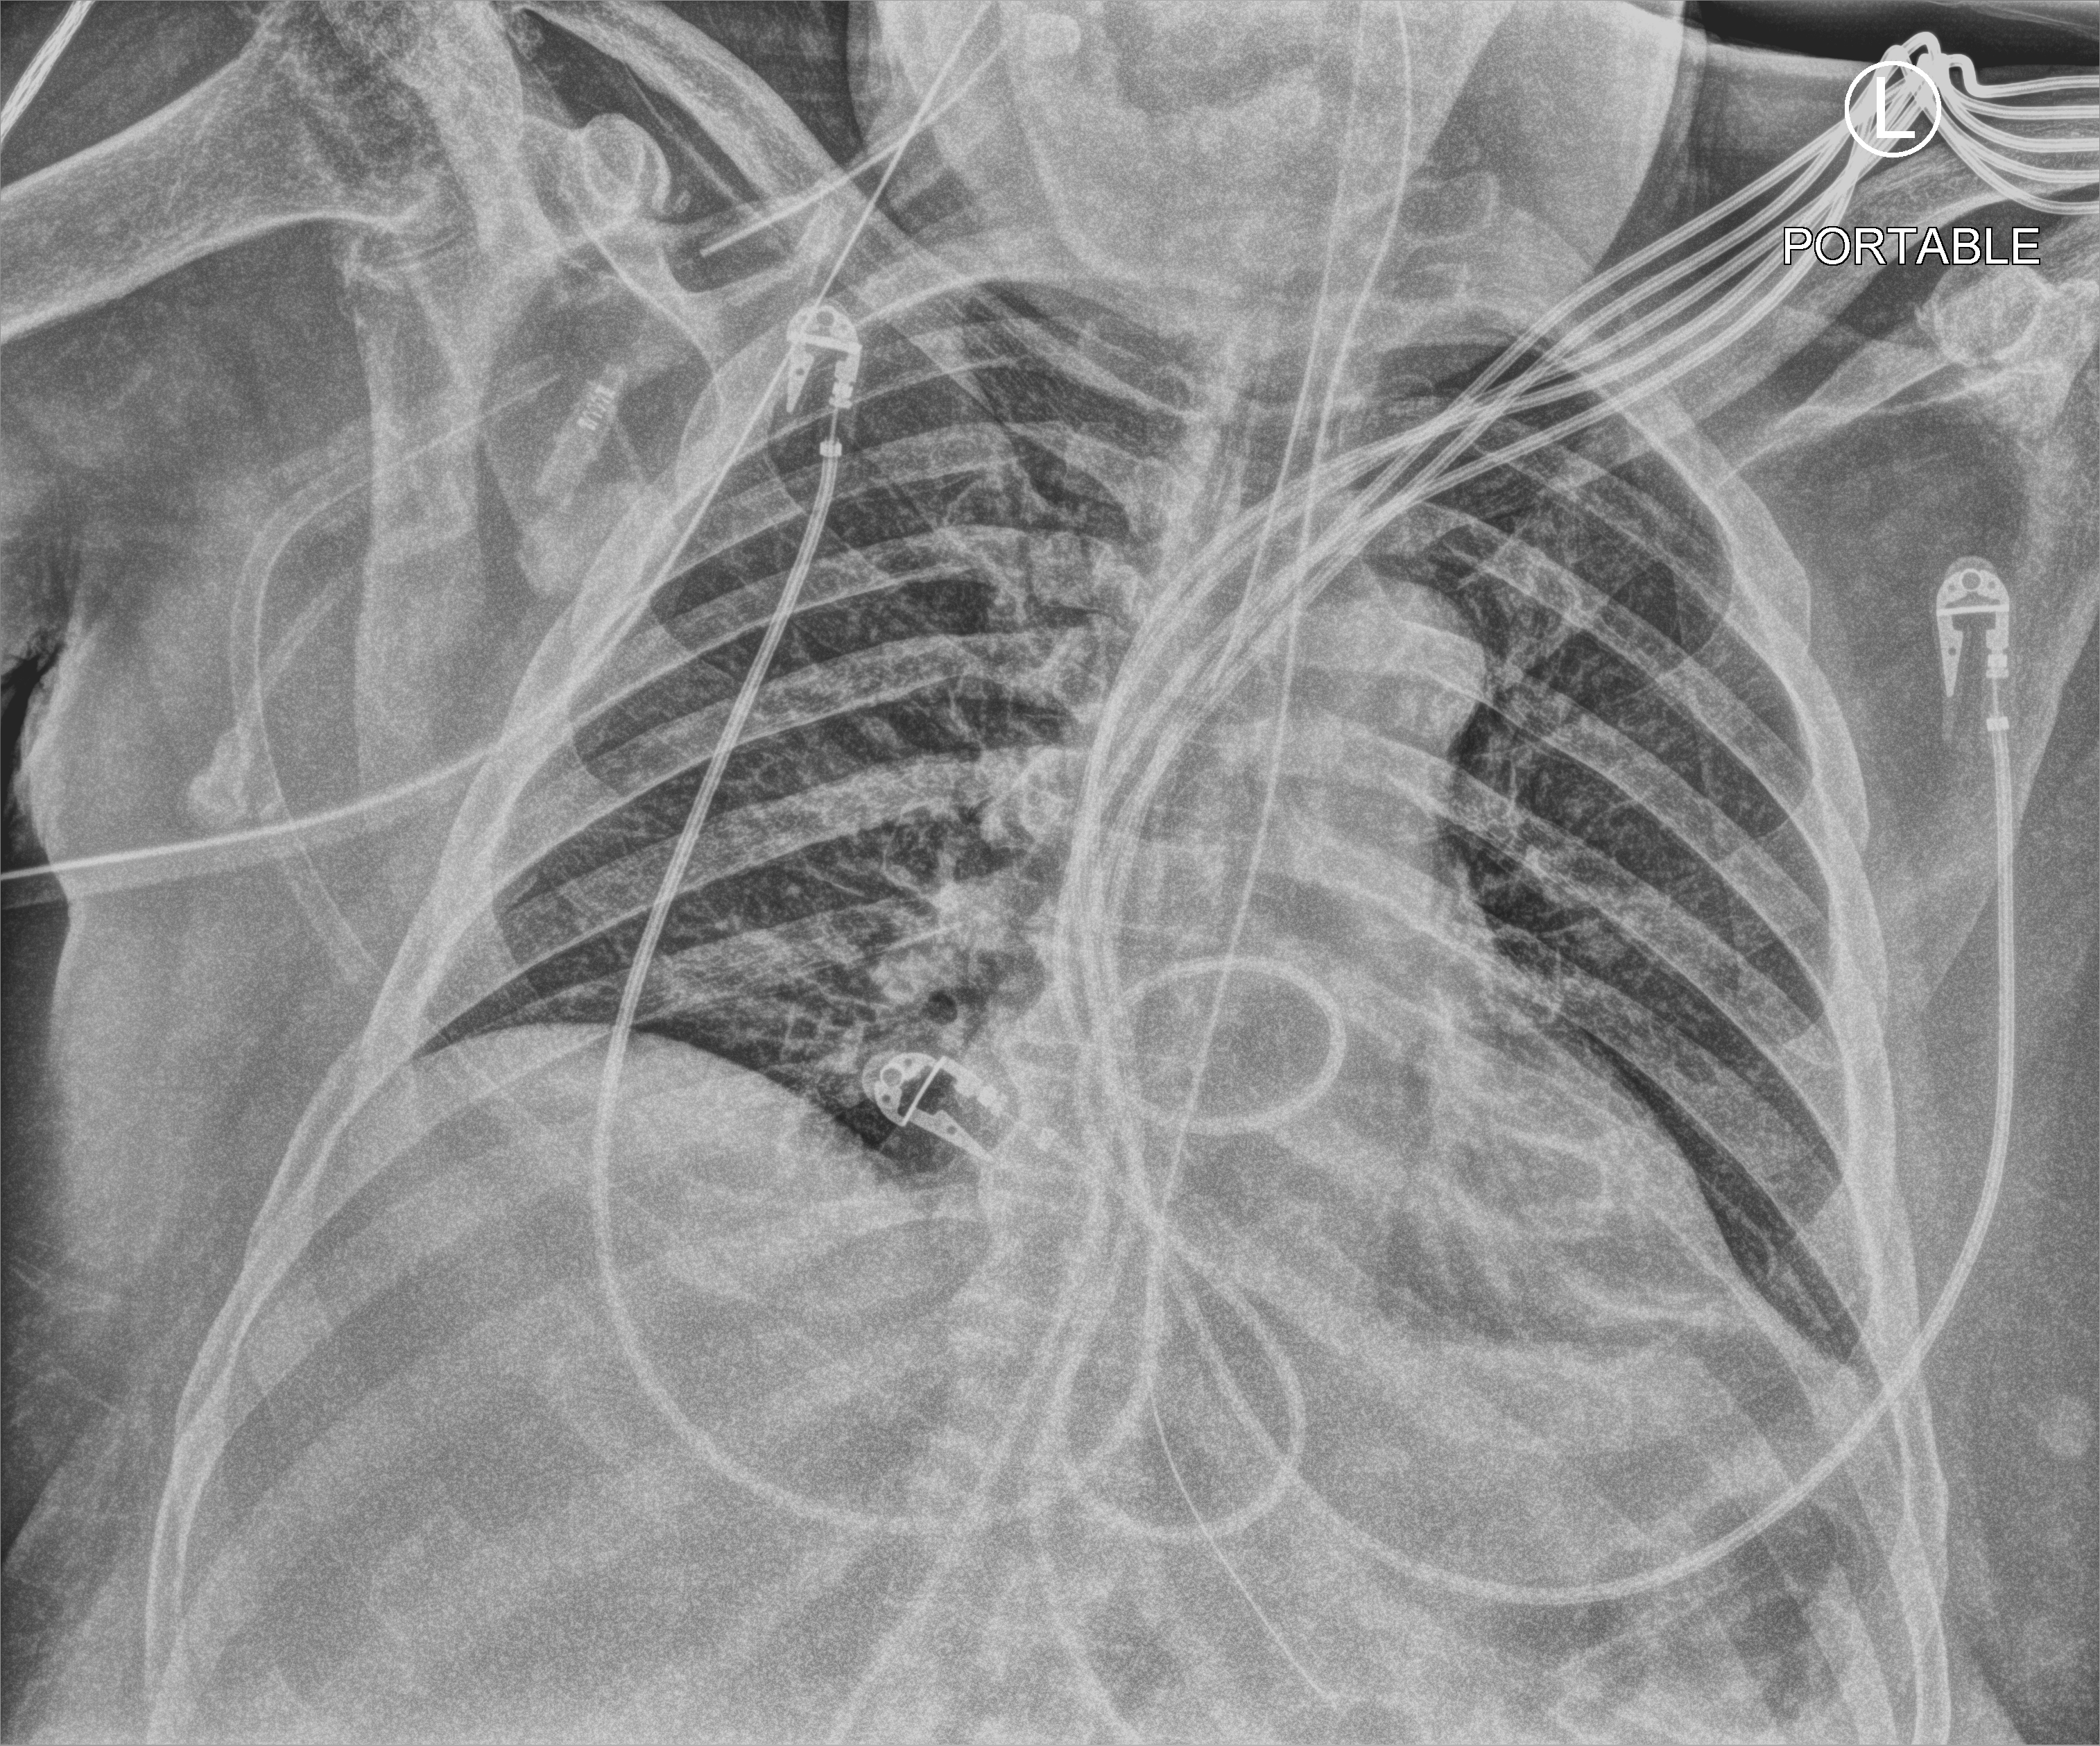
Bedside chest radiograph (computed radiography); anteroposterior (AP) projection. Patient hospitalised with COVID-19; male, aged 75–90 years.
Hospital-stay facts (about this admission, not read from this image; timing relative to this image not recorded): other chronic lung disease (admission record): no; admitted to intensive care during this hospital stay: yes; mechanically ventilated during this hospital stay: yes.